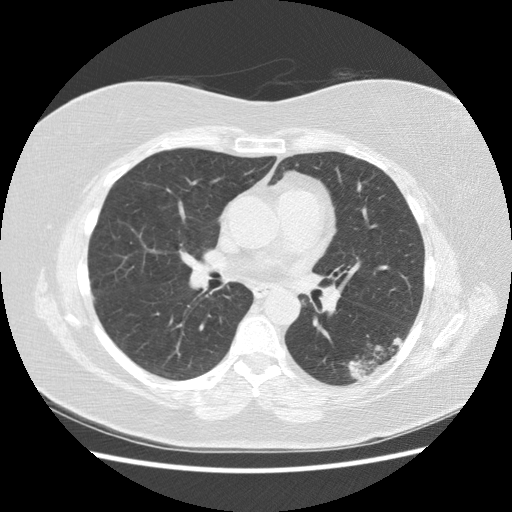
Low-dose screening chest CT, one axial slice; slice 83 of 151 in the series (ordered by position); reconstruction kernel STANDARD; 120 kVp; lung window (W 1500 / L -600 HU); 2.5 mm slice thickness; 512 × 512 image matrix.
Annotated regions visible in this slice (outlined manually by an expert reader):
- lesion 1 (tumor, lower lobe of left lung): bounding box (x1, y1, x2, y2) in pixels: (348, 336, 404, 380)